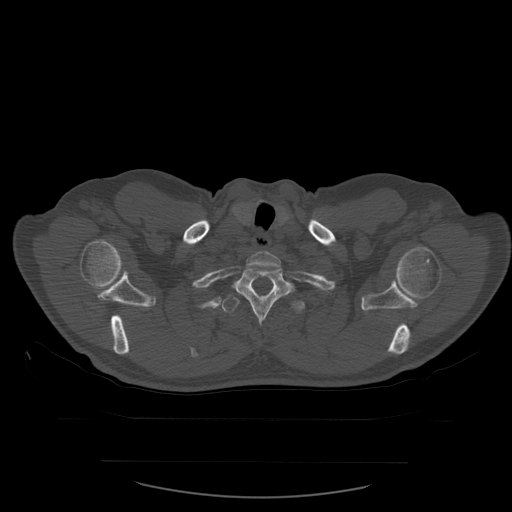
CT including the spine, one axial slice; position 474 of 590 along the scan axis; bone window (W 1800 / L 400 HU); 1.25 mm slice thickness; 512 × 512 image matrix, field of view 479 × 479 mm. Patient age 71 years. From the clinical record (not read from this slice): primary cancer: lung; vertebrae with lytic lesions (as recorded): T1, T2, L5, S1.
Annotated regions visible in this slice (semi-automatic segmentation, software-assisted and operator-edited):
- T1 vertebra: bounding box (x1, y1, x2, y2) in pixels: (247, 251, 282, 271)
- T2 vertebra: (234, 266, 294, 324)
- T3 vertebra: (222, 295, 306, 315)